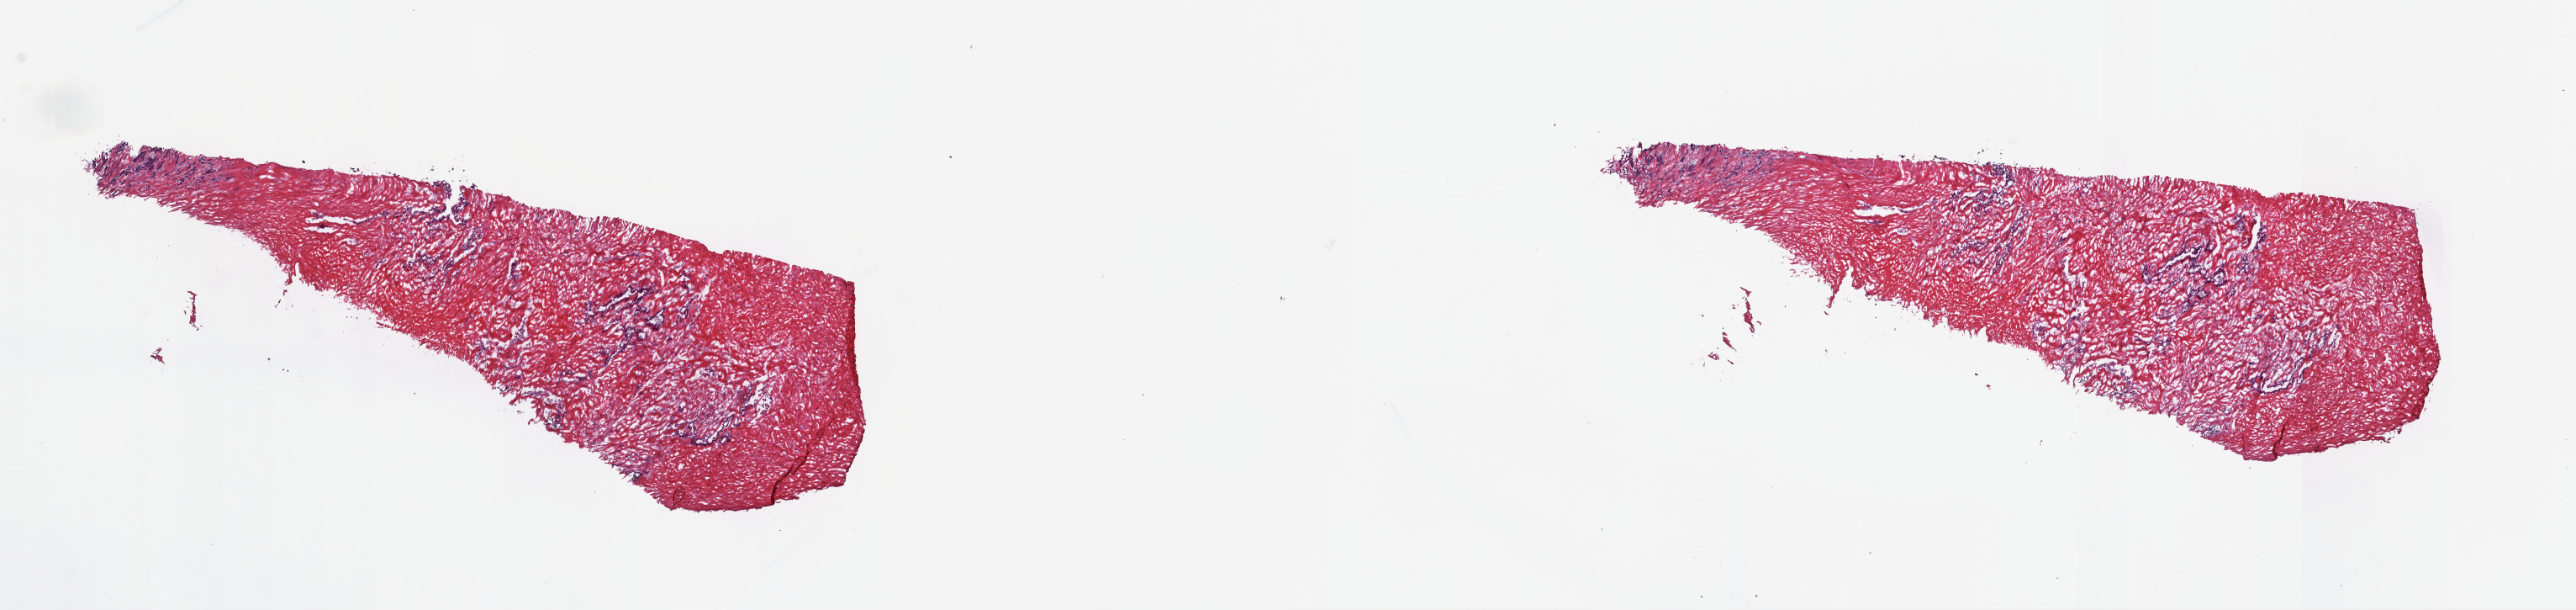
H&E whole-slide image, low-resolution overview of the scanned area, about 24.1 x 5.7 mm. Frozen section from the top of the tissue portion. Primary tumour sample from the mesothelium. Male patient; age at initial diagnosis 75 years. Composition of this section per pathologist review: tumour cells 100%, tumour nuclei 70%, normal cells 0%, stromal cells 0%, necrosis 0%. Infiltration values recorded for this section: lymphocyte infiltration 0%, monocyte infiltration 0%, neutrophil infiltration 0%.
Pathologic diagnosis: Epithelioid mesothelioma, malignant (pleura, NOS). AJCC pathologic stage: II.